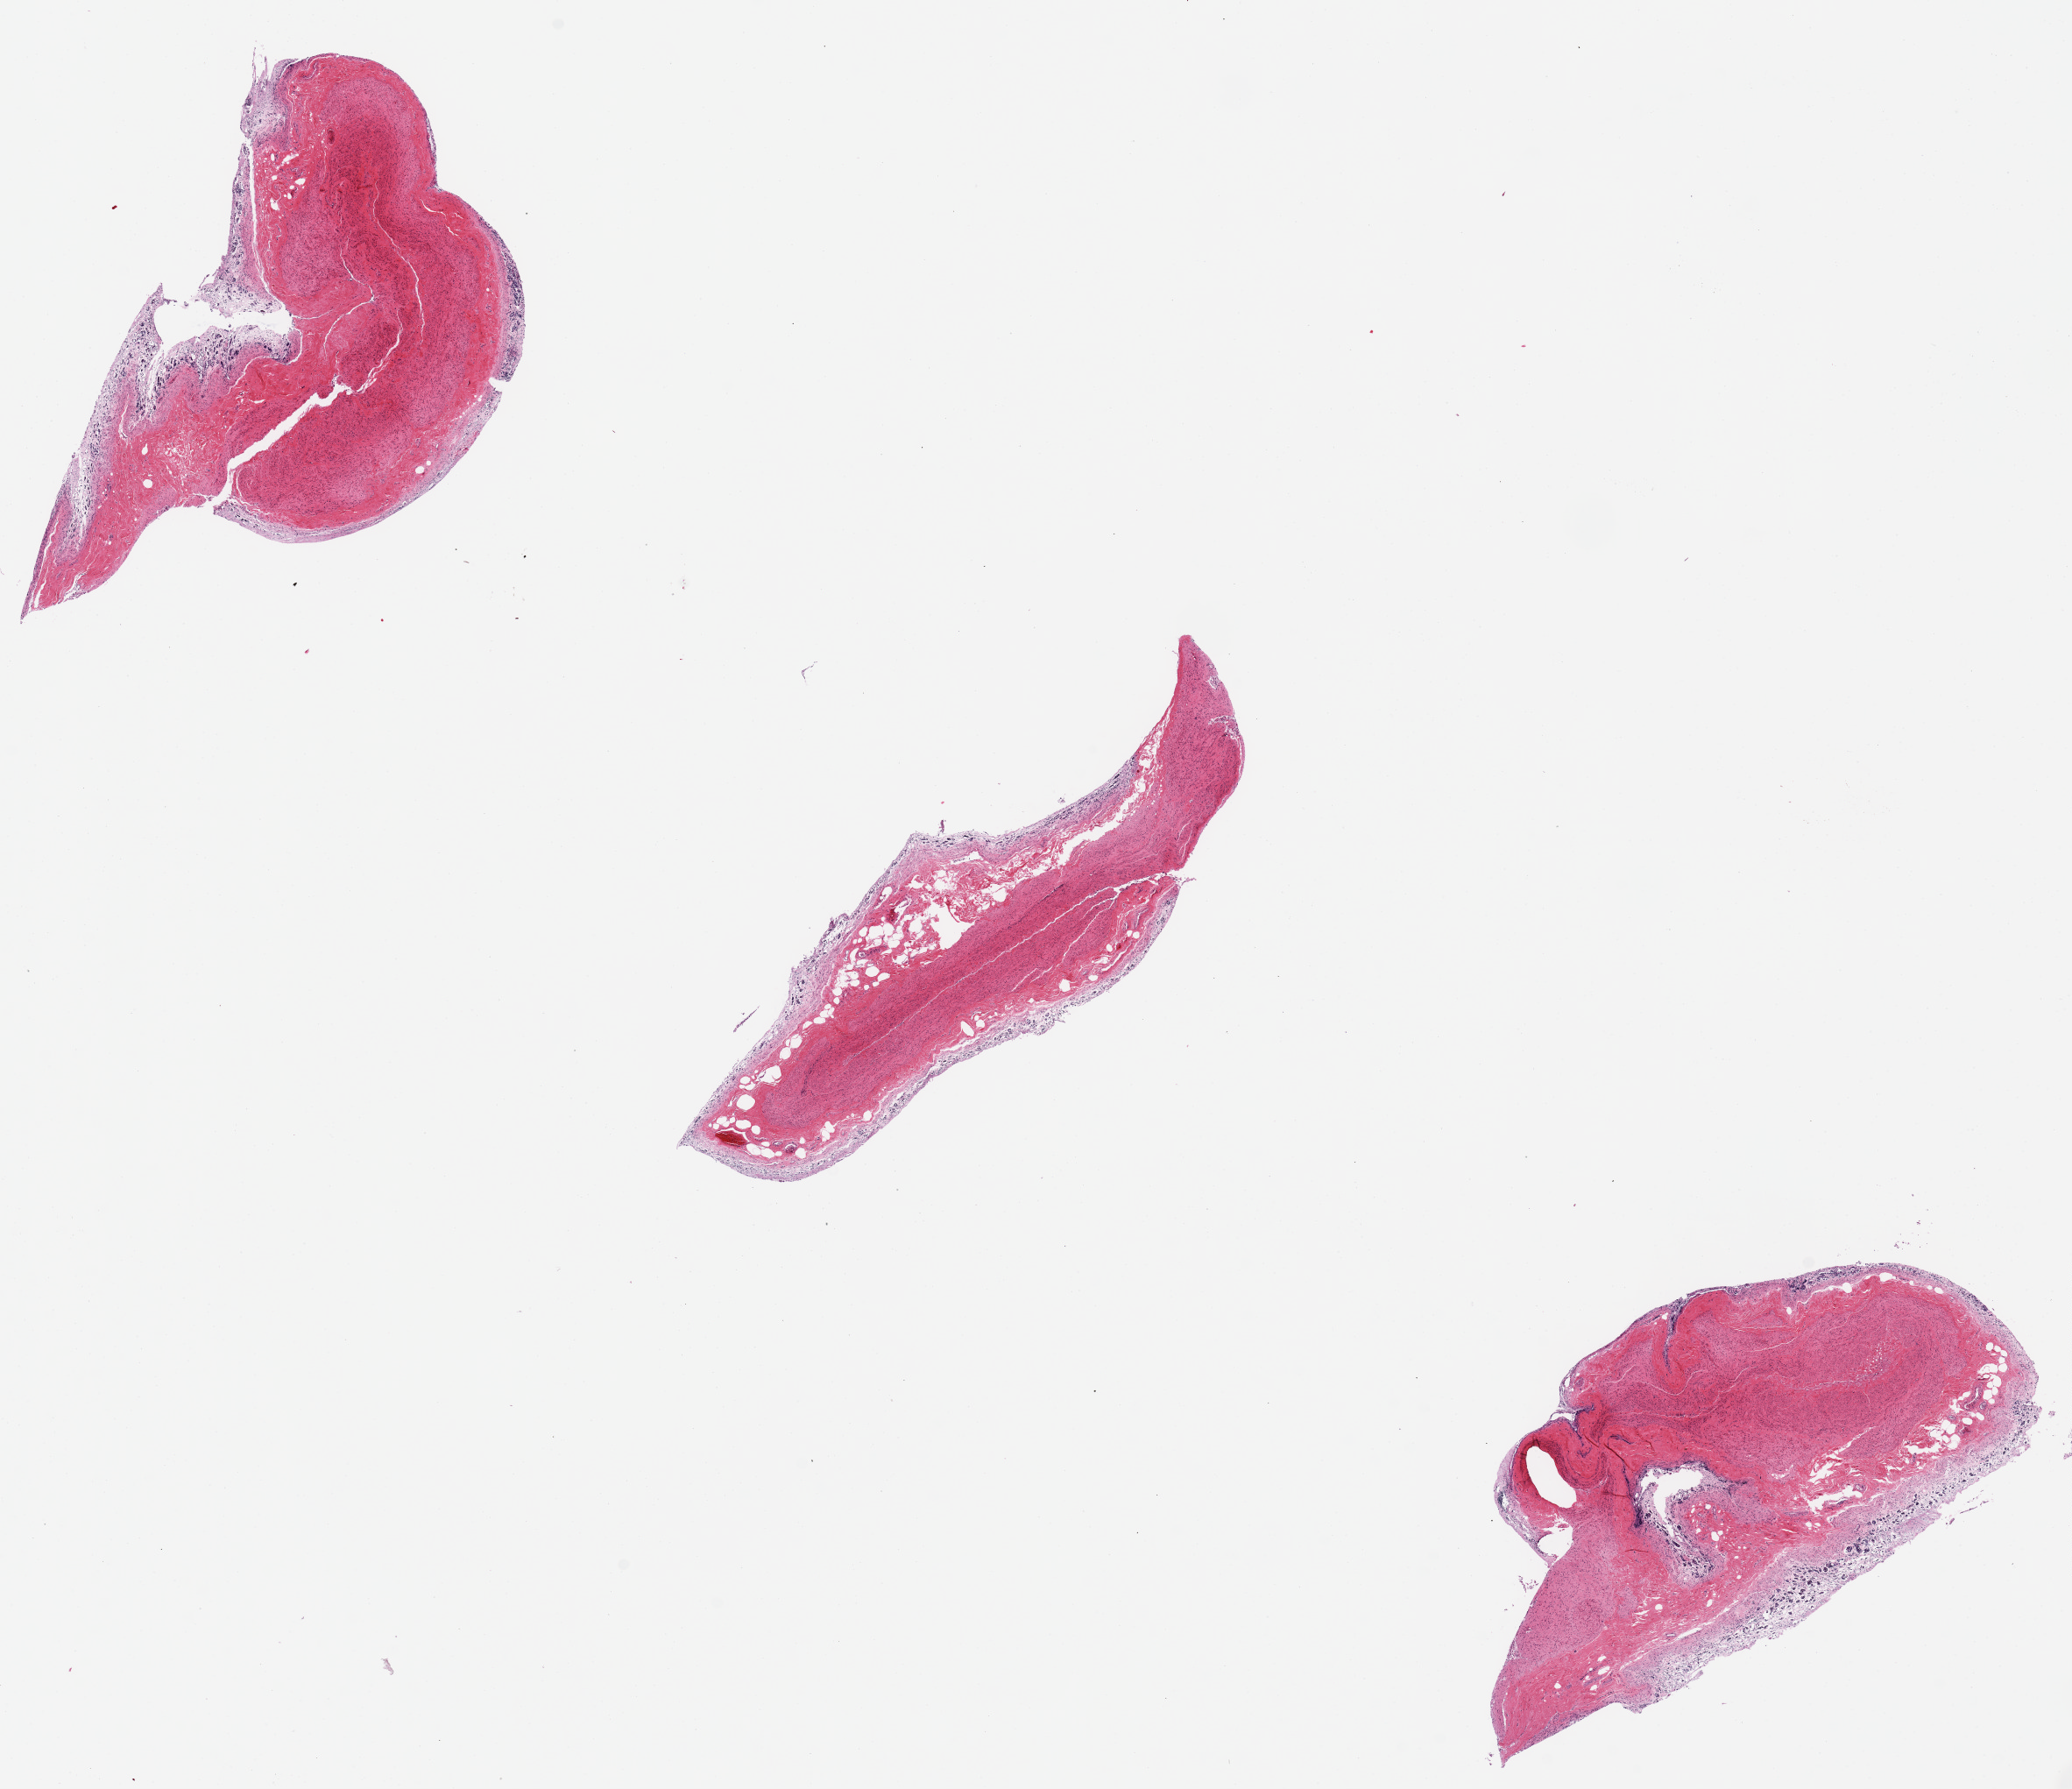
Whole-slide image, haematoxylin and eosin stain — whole scanned area (about 18.7 x 16.1 mm, acquisition: 20x scan) shown as a low-resolution overview, PAXgene-fixed, paraffin-embedded tissue, sampled site (target tissue): stomach, tissue donor sample. Donor sex: male.
Pathologist's review note for this sample: too autolyzed for mucosal study.